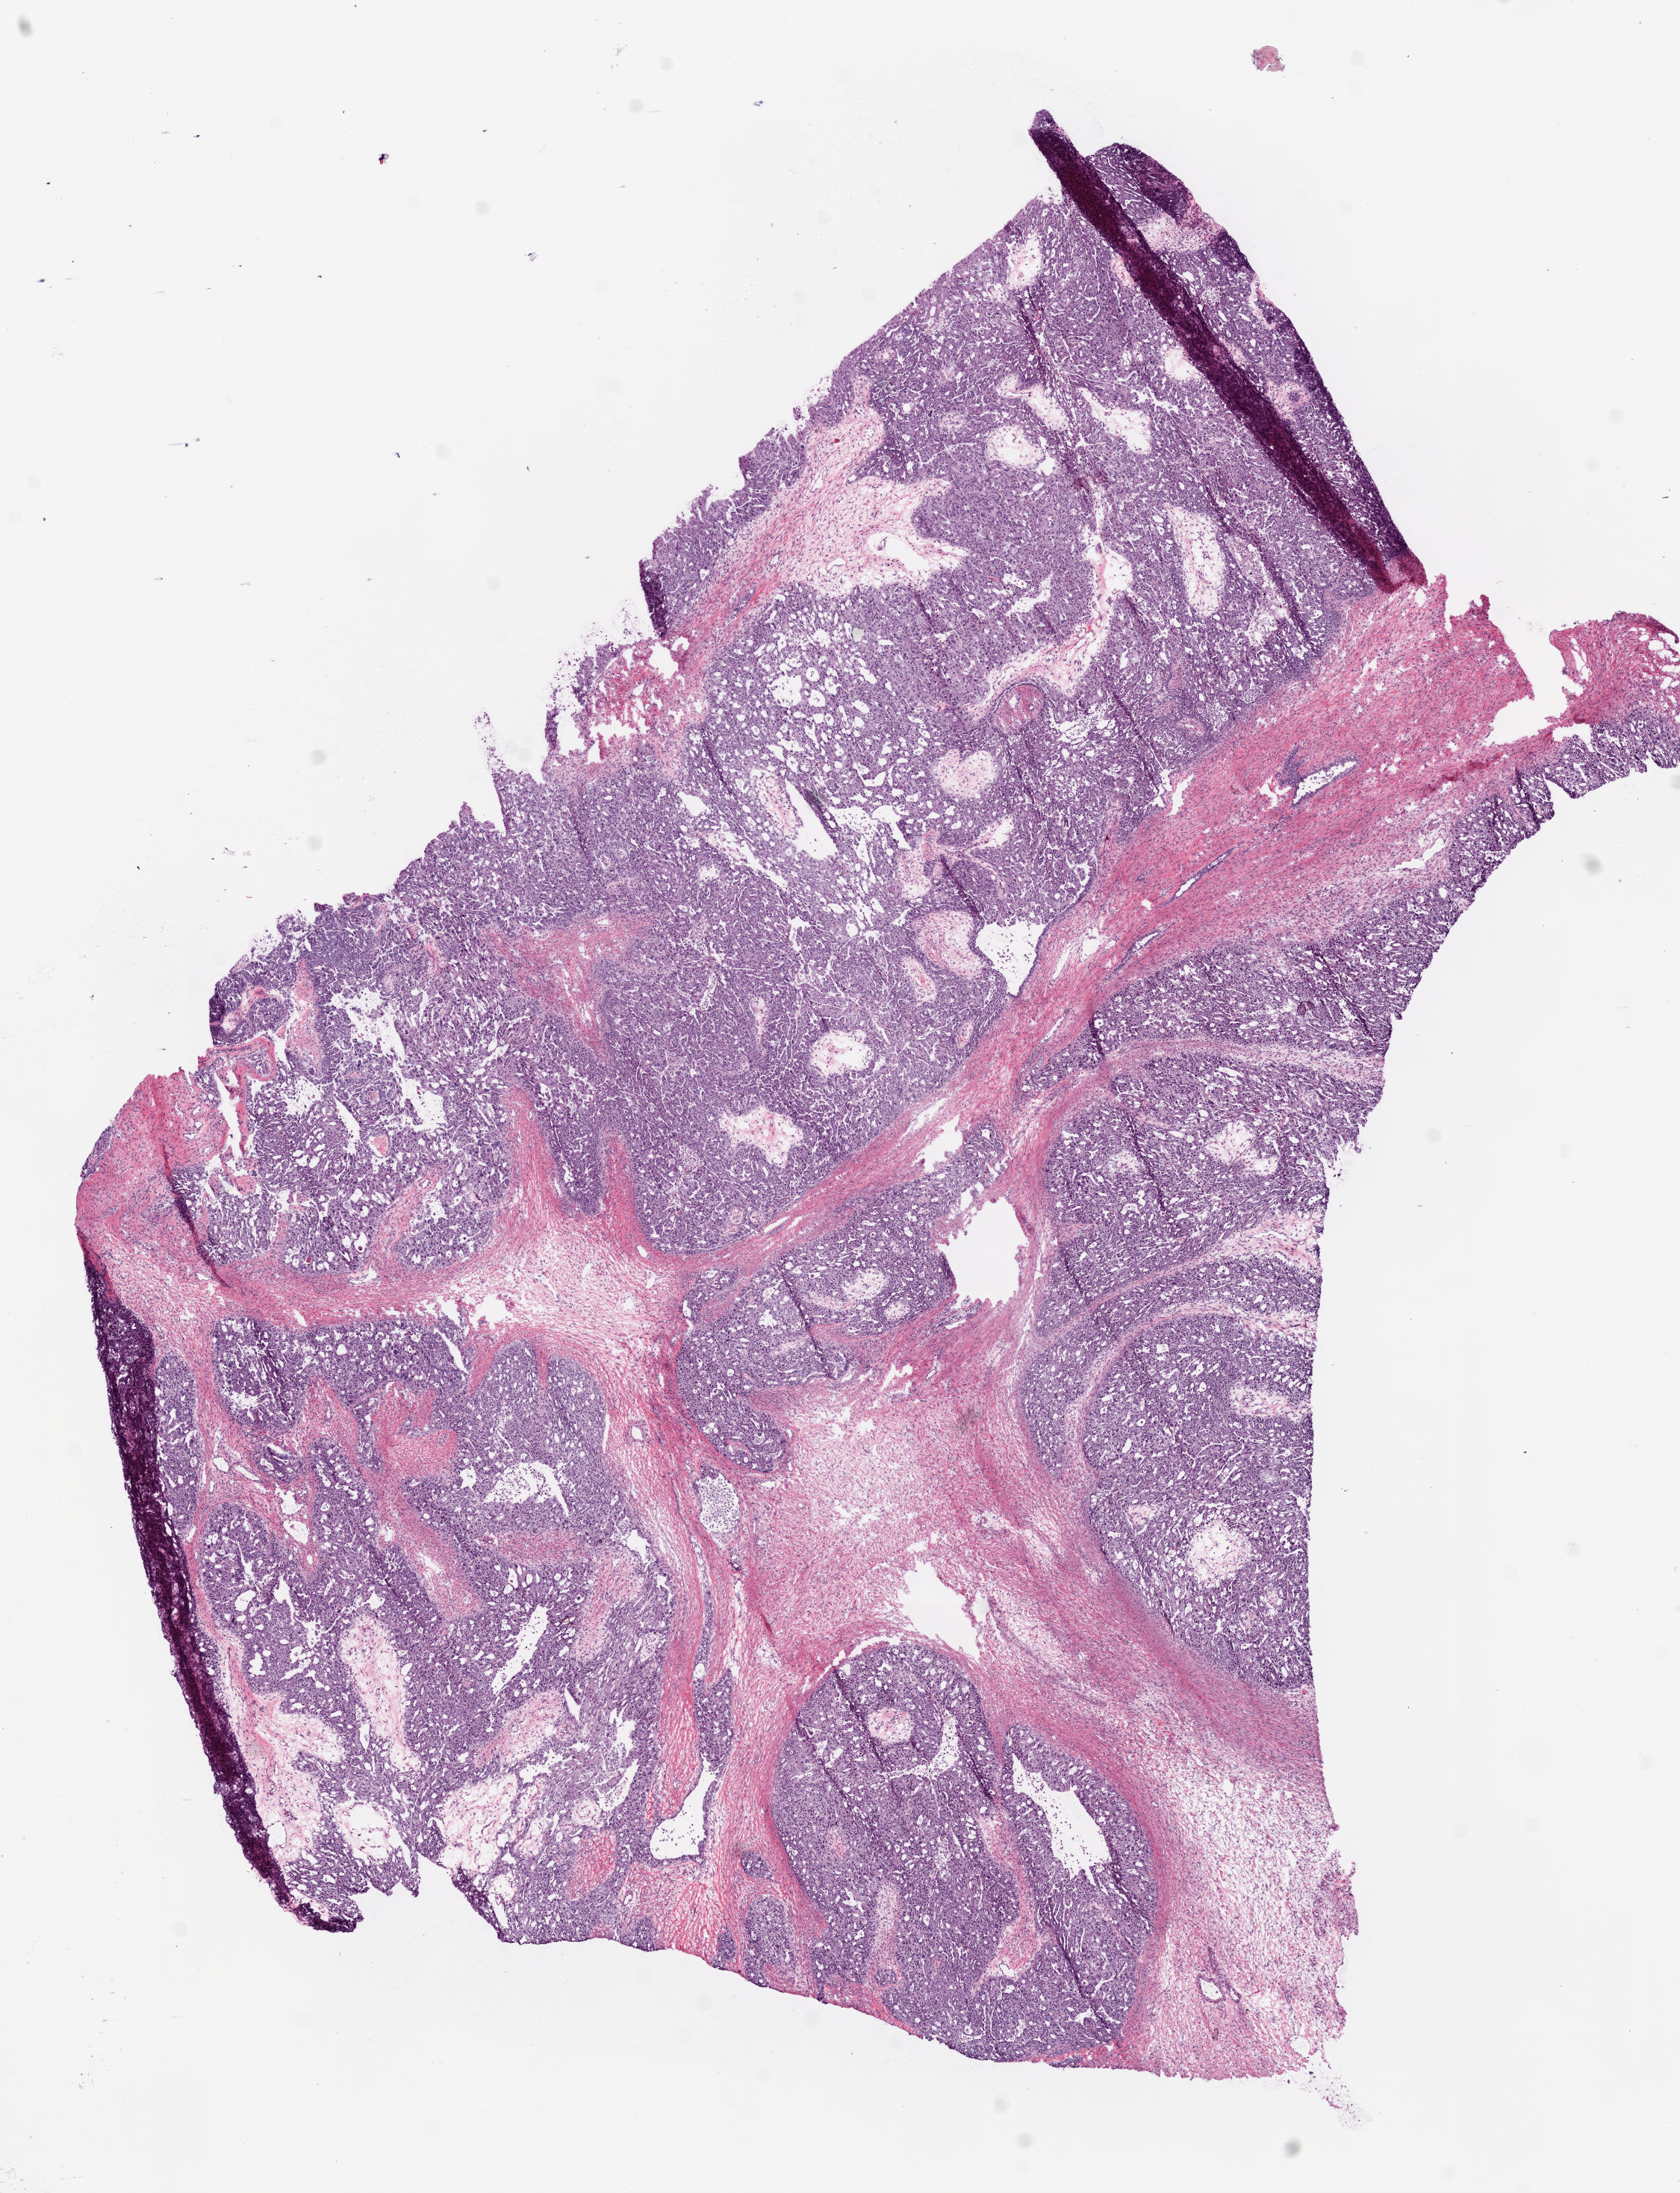
Digitized H&E tissue section (whole slide) — low-resolution overview of the scanned area, about 9.0 x 11.8 mm; frozen section from the bottom of the tissue portion; primary tumour sample from the ovary. Female, age 55 years at initial diagnosis. Histologic grade: G3 (poorly differentiated). Slide review estimates, as recorded: tumour cells 70%, tumour nuclei 80%, normal cells 0%, stromal cells 25%, necrosis 5%.
Laterality: right. Histologic diagnosis: Serous cystadenocarcinoma, NOS. FIGO stage: IIIC.